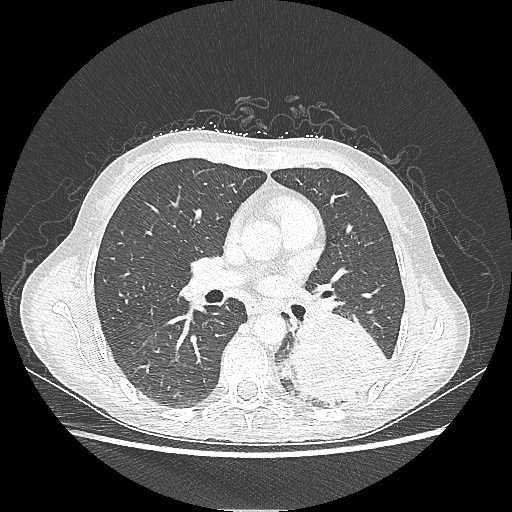
Chest CT, one axial slice; slice 120 of 220 in the series (ordered by position); reconstruction kernel LUNG; 80 kVp; lung window (W 1500 / L -600 HU); 1.25 mm slice thickness; 512 × 512 image matrix, field of view 360 × 360 mm. Female patient, age 53 years. From the clinical record (not read from this slice): clinical TNM (as recorded): T3 N0 M0.
Outlined on this slice (bounding box drawn by a radiologist):
- lung tumour (recorded histology: adenocarcinoma): bounding box <289,314,390,403> (left, top, right, bottom; pixels)